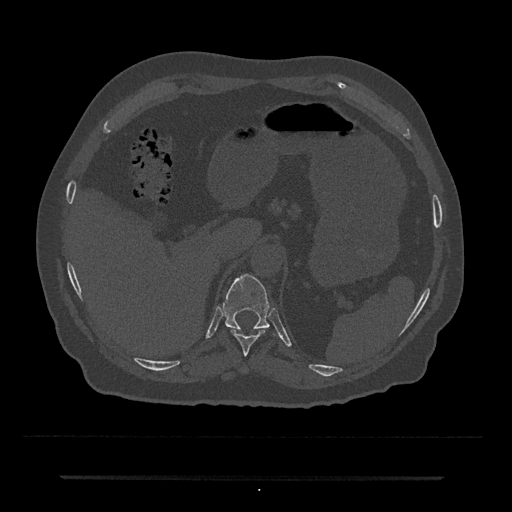
CT including the spine, one axial slice; position 202 of 797 along the scan axis; reconstruction kernel Br40s/3; bone window (W 1800 / L 400 HU); 0.5 mm slice thickness; 512 × 512 image matrix, field of view 437 × 437 mm. Male patient, age 69 years. From the clinical record (not read from this slice): primary cancer: prostate.
Structures marked on this image (semi-automatically segmented with operator editing):
- T10 vertebra: bounding box <230,329,266,356> (left, top, right, bottom; pixels)
- T11 vertebra: <222,274,279,334>